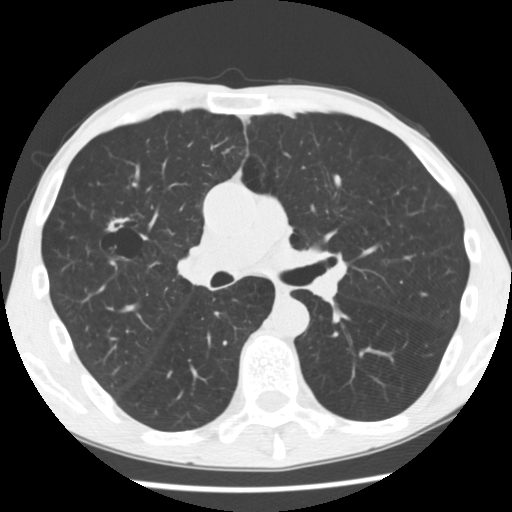
Axial slice from a low-dose chest CT screening exam, baseline screening round, lung window (W 1500 / L -600 HU), standard (soft-tissue) reconstruction kernel (STANDARD), 120 kVp, slice 129 of 292 in the series, 512 × 512 image matrix. Male participant, aged 56 years at enrolment. Current smoker at enrolment.
• Lesion marked by an expert reader, bounding box <96,206,155,257> (left, top, right, bottom; pixels).
• The screening reader recorded 2 non-calcified nodules or masses ≥4 mm on this exam (right upper lobe, right upper lobe); which of them this box marks is not recorded.
• Lung cancer was diagnosed 476 days after this screen (after the second annual screen): squamous cell carcinoma, NOS, right upper lobe, right middle lobe, well differentiated (G1), stage IA (AJCC 6th edition), 27 mm at pathology.